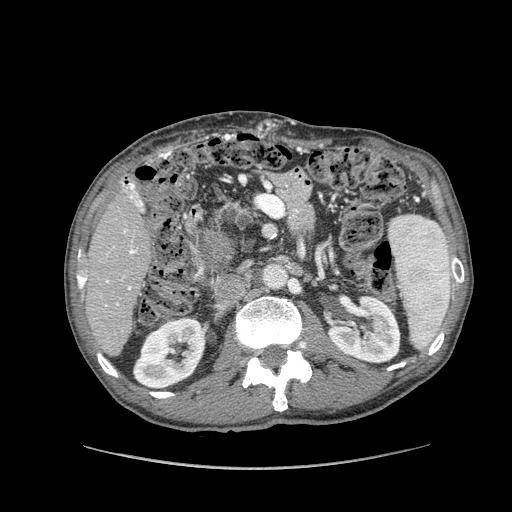
Contrast-enhanced abdominal CT (liver protocol), one axial slice. Slice 41 of 162 in the series (ordered by position). Reconstruction kernel STANDARD. Soft-tissue window (W 400 / L 40 HU). 2.5 mm slice thickness. 512 × 512 image matrix, field of view 400 × 400 mm. Case-level facts recorded for this patient, not image findings: diagnosis: hepatocellular carcinoma (patient treated with transarterial chemoembolisation; whether this scan precedes or follows treatment is not stated here); TNM stage (as recorded): Stage-IIIA.
Annotated regions visible in this slice (semi-automatically segmented with operator editing):
- liver parenchyma outside the tumour (the mass and vessels are separate outlines, so this box may not span the whole liver): box from (x=84, y=182) to (x=151, y=356) px
- liver vessels: (x=106, y=183)–(x=143, y=290)